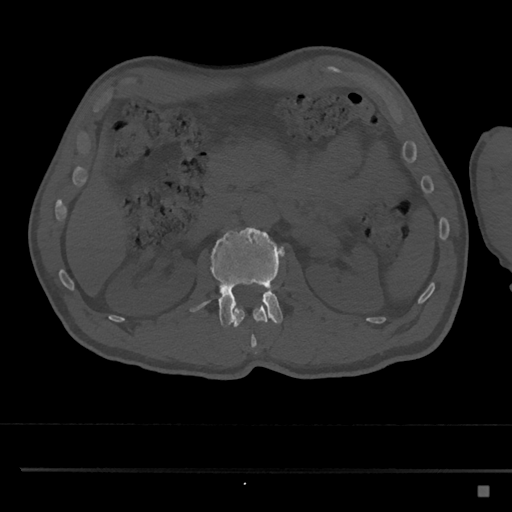
CT including the spine, one axial slice; slice 785 of 797 in the series (ordered by position); reconstruction kernel Br40s/3; 120 kVp; bone window (W 1800 / L 400 HU); 0.5 mm slice thickness; 512 × 512 image matrix. Male patient, age 59 years. From the clinical record (not read from this slice): primary cancer: prostate.
Structures marked on this image (semi-automatic segmentation, software-assisted and operator-edited):
- L1 vertebra: bounding box (x1, y1, x2, y2) in pixels: (233, 301, 268, 347)
- L2 vertebra: (189, 227, 285, 327)